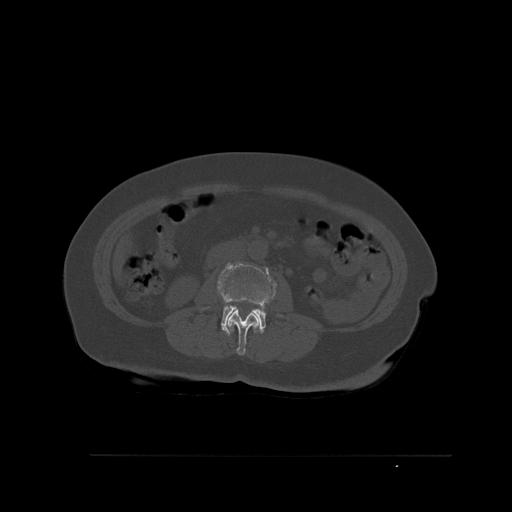
CT including the spine, one axial slice; position 235 of 527 along the scan axis; bone window (W 1800 / L 400 HU); 512 × 512 image matrix. Female patient, age 73 years. Case-level facts recorded for this patient, not image findings: primary cancer: breast.
Outlined on this slice (semi-automatically segmented with operator editing):
- L2 vertebra: bounding box [x1, y1, x2, y2] px = [226, 309, 259, 355]
- L3 vertebra: [217, 261, 277, 336]
- L4 vertebra: [246, 314, 259, 333]